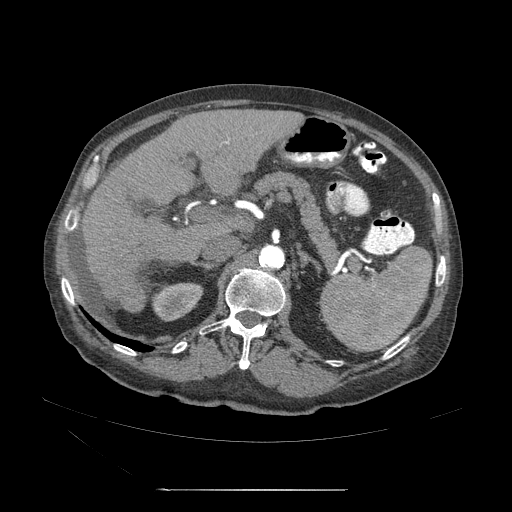
Contrast-enhanced abdominal CT (liver protocol), one axial slice. Position 24 of 71 along the scan axis. Reconstruction kernel STANDARD. 120 kVp. Soft-tissue window (W 400 / L 40 HU). 512 × 512 image matrix, field of view 440 × 440 mm. Case-level facts recorded for this patient, not image findings: diagnosis: hepatocellular carcinoma (patient treated with transarterial chemoembolisation; whether this scan precedes or follows treatment is not stated here); TNM stage (as recorded): Stage-II; Child-Pugh class: A.
Outlined on this slice (semi-automatic segmentation, software-assisted and operator-edited):
- abdominal aorta: bounding box [x1, y1, x2, y2] px = [260, 244, 286, 272]
- liver parenchyma outside the tumour (the mass and vessels are separate outlines, so this box may not span the whole liver): [83, 112, 293, 315]
- liver vessels: [183, 158, 241, 264]